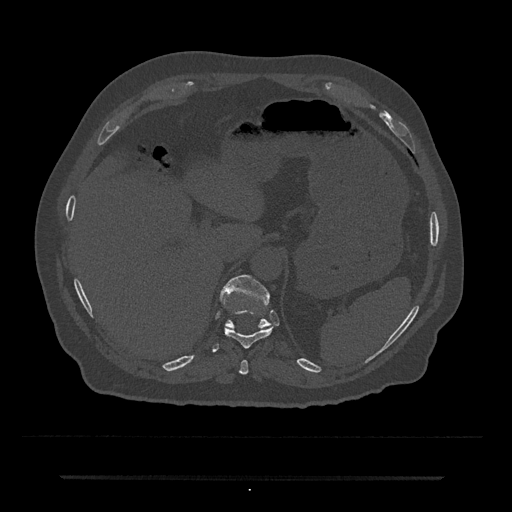
CT including the spine, one axial slice; reconstruction kernel Br40s/3; 120 kVp; bone window (W 1800 / L 400 HU); 512 × 512 image matrix, field of view 437 × 437 mm. Male patient, age 69 years. From the clinical record (not read from this slice): primary cancer: prostate.
Outlined on this slice (semi-automatic segmentation, software-assisted and operator-edited):
- T10 vertebra: bounding box <212,310,274,353> (left, top, right, bottom; pixels)
- T11 vertebra: <219,275,271,329>
- T9 vertebra: <239,360,249,375>